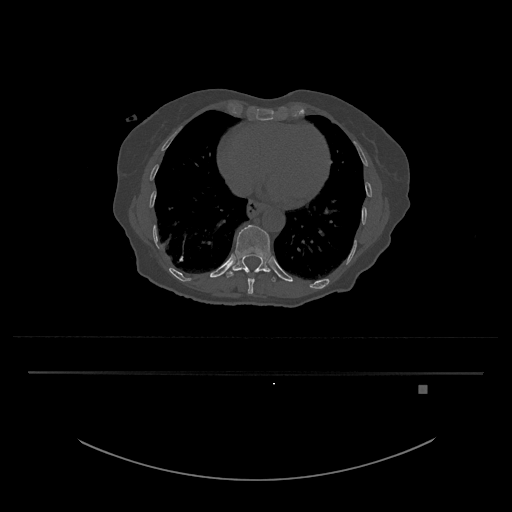
CT including the spine, one axial slice; position 682 of 797 along the scan axis; reconstruction kernel Br40s/3; bone window (W 1800 / L 400 HU); 0.5 mm slice thickness; 512 × 512 image matrix, field of view 500 × 500 mm. Patient: female, 57 years. From the clinical record (not read from this slice): primary cancer: cervical.
Structures marked on this image (semi-automatically segmented with operator editing):
- T10 vertebra: box from (x=244, y=270) to (x=259, y=294) px
- T11 vertebra: (x=226, y=225)–(x=276, y=282)